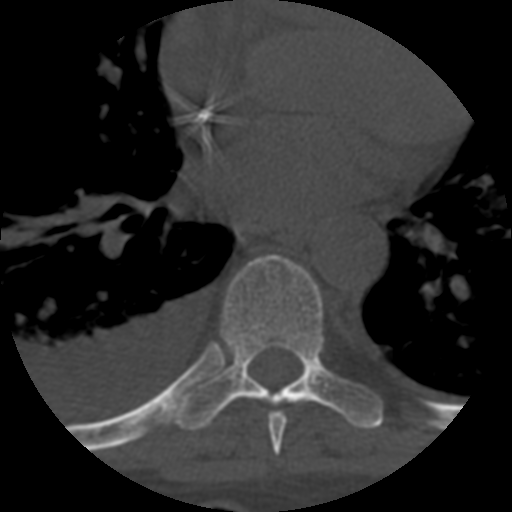
CT including the spine, one axial slice; slice 401 of 708 in the series (ordered by position); 120 kVp; one of 3 acquisitions stored at this slice position; bone window (W 1800 / L 400 HU); 512 × 512 image matrix, field of view 160 × 160 mm. Patient age 55 years. Case-level facts recorded for this patient, not image findings: primary cancer: colon; vertebrae with lytic lesions (as recorded): T12, L1, L5.
Structures marked on this image (semi-automatic segmentation, software-assisted and operator-edited):
- T7 vertebra: bounding box (x1, y1, x2, y2) in pixels: (267, 412, 287, 455)
- T8 vertebra: (176, 255, 383, 431)